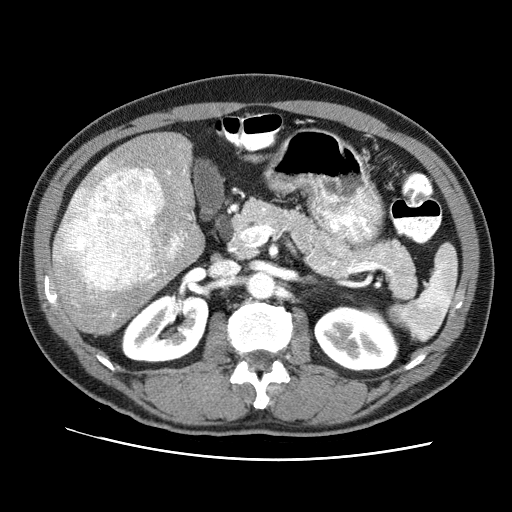
Contrast-enhanced abdominal CT (liver protocol), one axial slice; slice 38 of 71 in the series (ordered by position); 120 kVp; soft-tissue window (W 400 / L 40 HU); 512 × 512 image matrix, field of view 360 × 360 mm. Case-level facts recorded for this patient, not image findings: diagnosis: hepatocellular carcinoma (patient treated with transarterial chemoembolisation; whether this scan precedes or follows treatment is not stated here); TNM stage (as recorded): Stage-II; Child-Pugh class: A; tumour differentiation: well differentiated; tumour size: 4.6 cm.
Structures marked on this image (semi-automatic segmentation, software-assisted and operator-edited):
- liver parenchyma outside the tumour (the mass and vessels are separate outlines, so this box may not span the whole liver): box from (x=52, y=131) to (x=204, y=332) px
- mass: (x=52, y=165)–(x=164, y=291)
- liver vessels: (x=80, y=159)–(x=191, y=317)